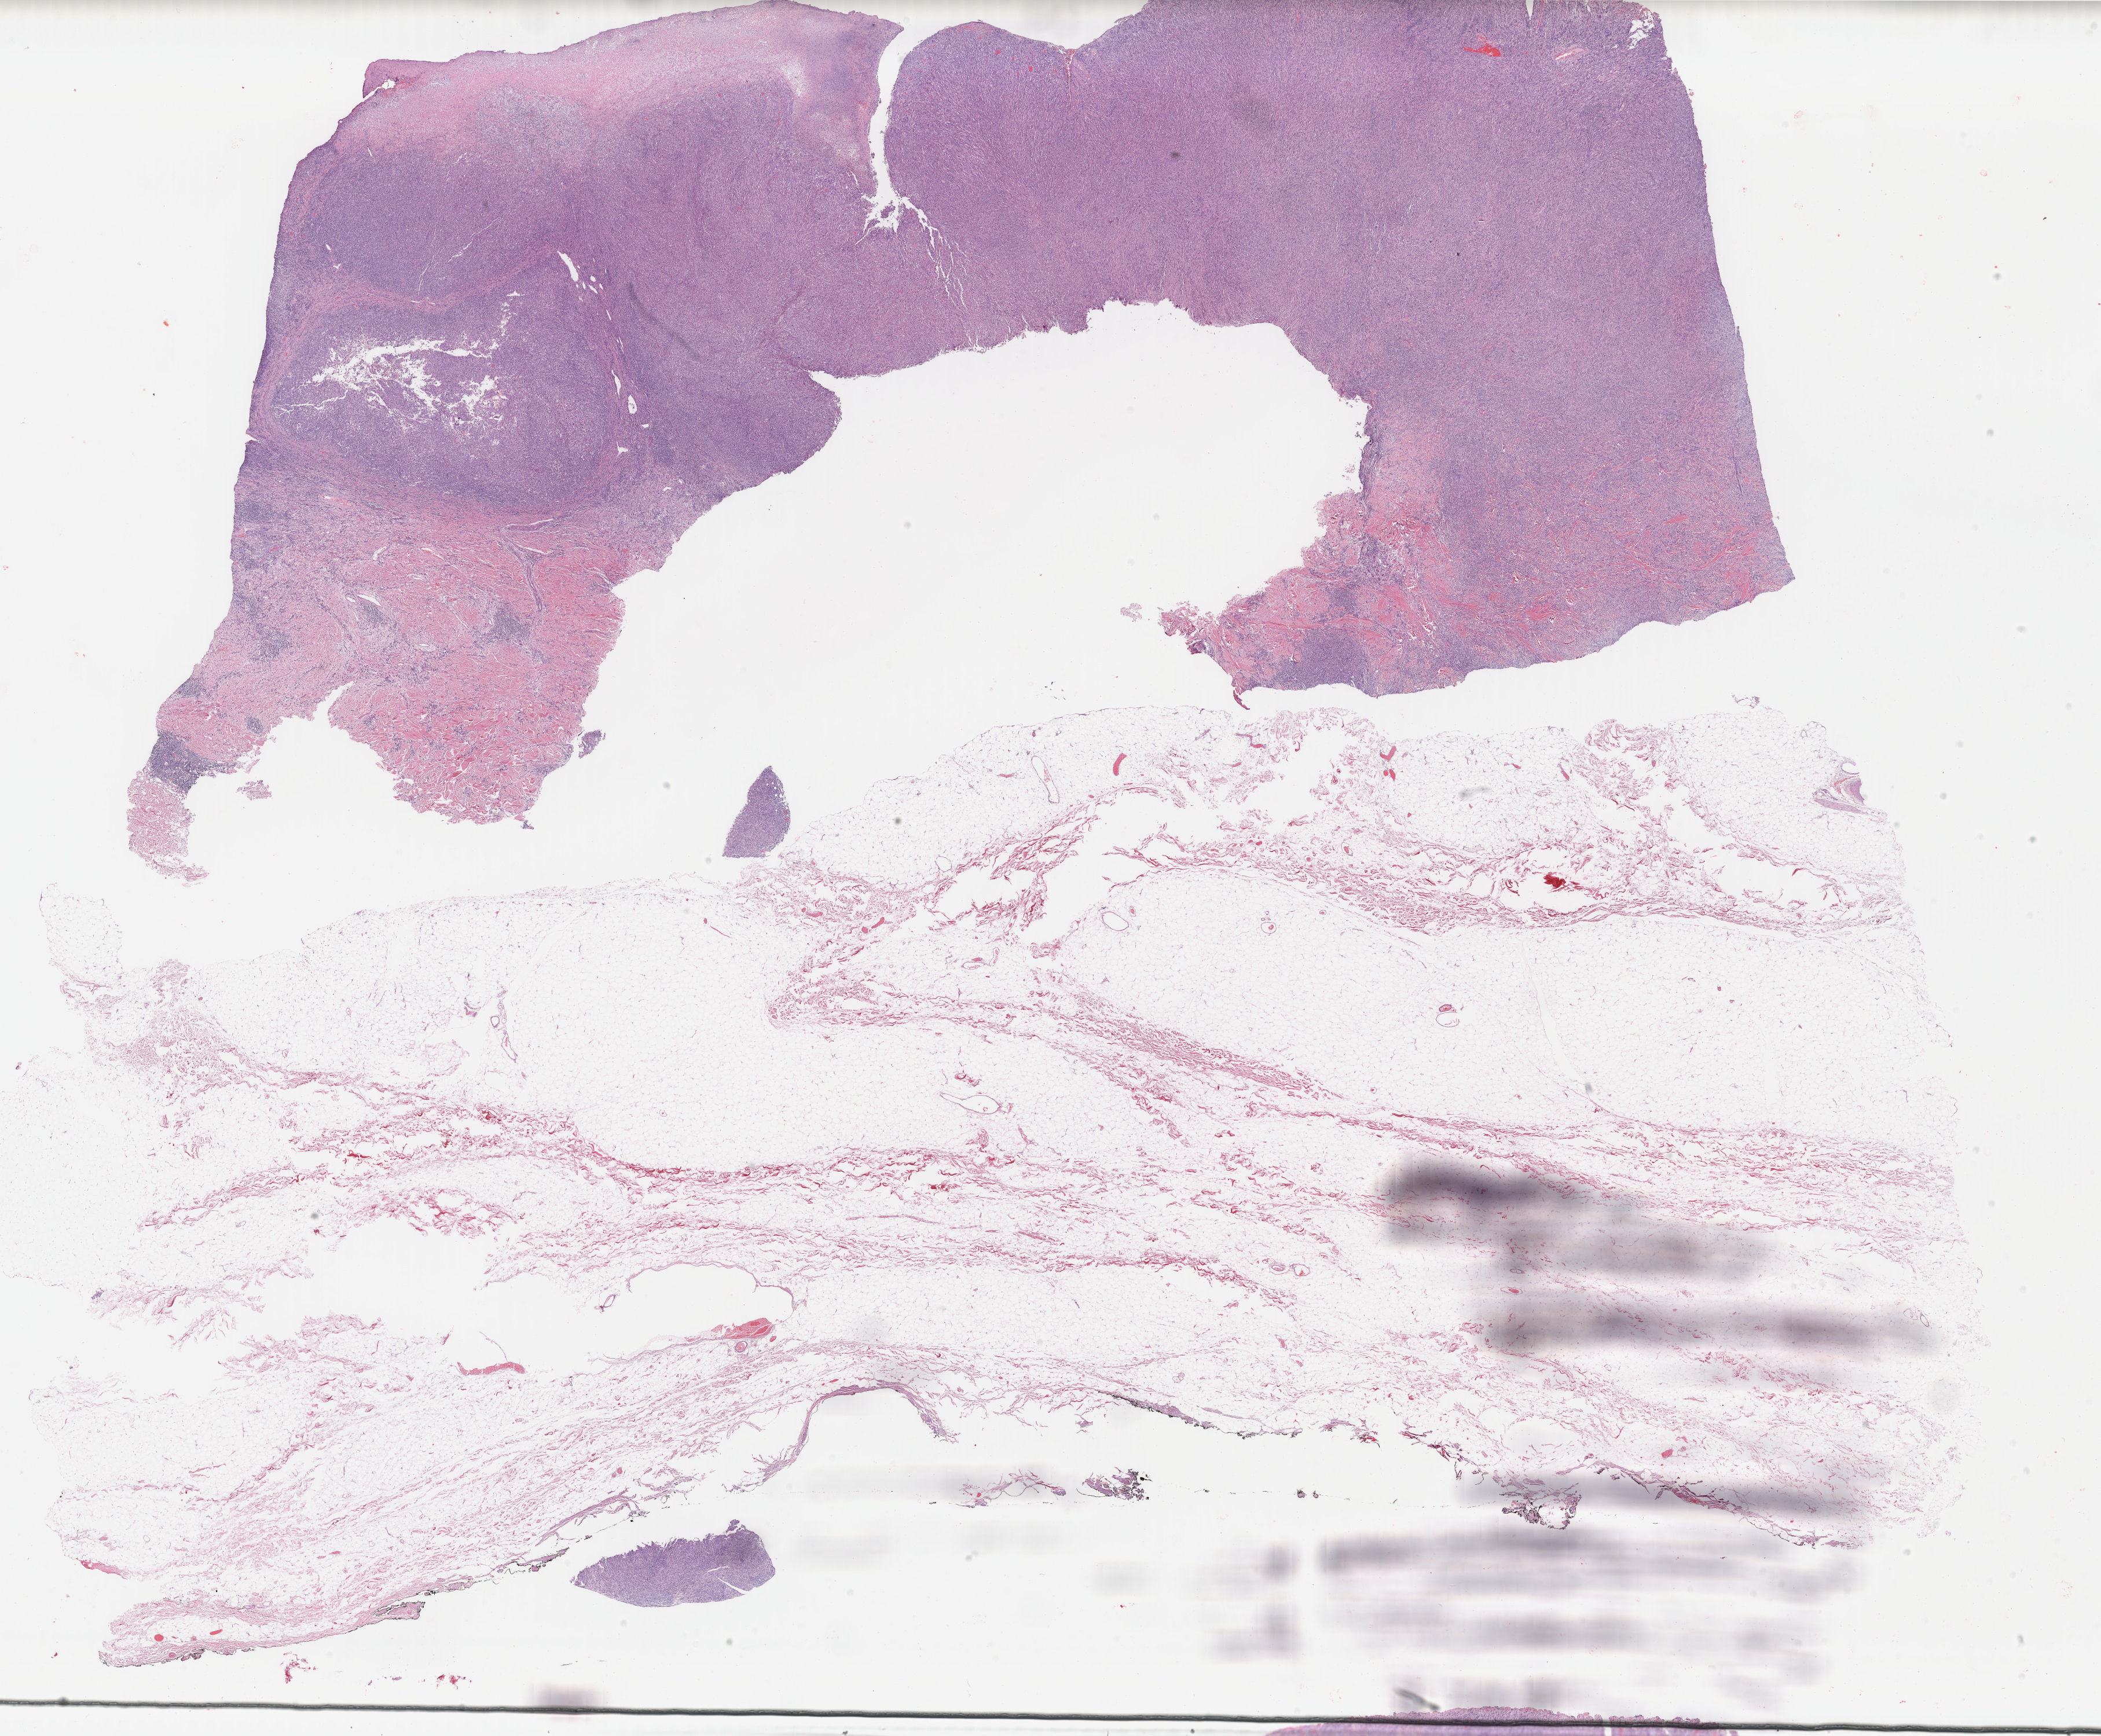
Whole-slide histology image, Hematoxylin and eosin (H&E) stained, whole scanned area (about 28.8 x 23.8 mm, acquisition: 40x scan) shown as a low-resolution overview; formalin-fixed paraffin-embedded (FFPE) diagnostic section; primary tumour sample from the skin. Male, age 77 years at initial diagnosis.
• diagnosis: Spindle cell melanoma, NOS